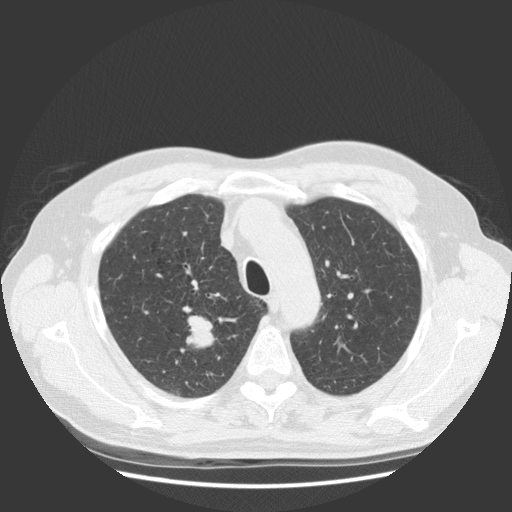
Low-dose screening chest CT, one axial slice; position 98 of 131 along the scan axis; lung window (W 1500 / L -600 HU); 2.5 mm slice thickness; 512 × 512 image matrix.
Outlined on this slice (expert manual segmentation):
- lesion 1 (tumor, upper lobe of right lung): bounding box <186,316,217,348> (left, top, right, bottom; pixels)